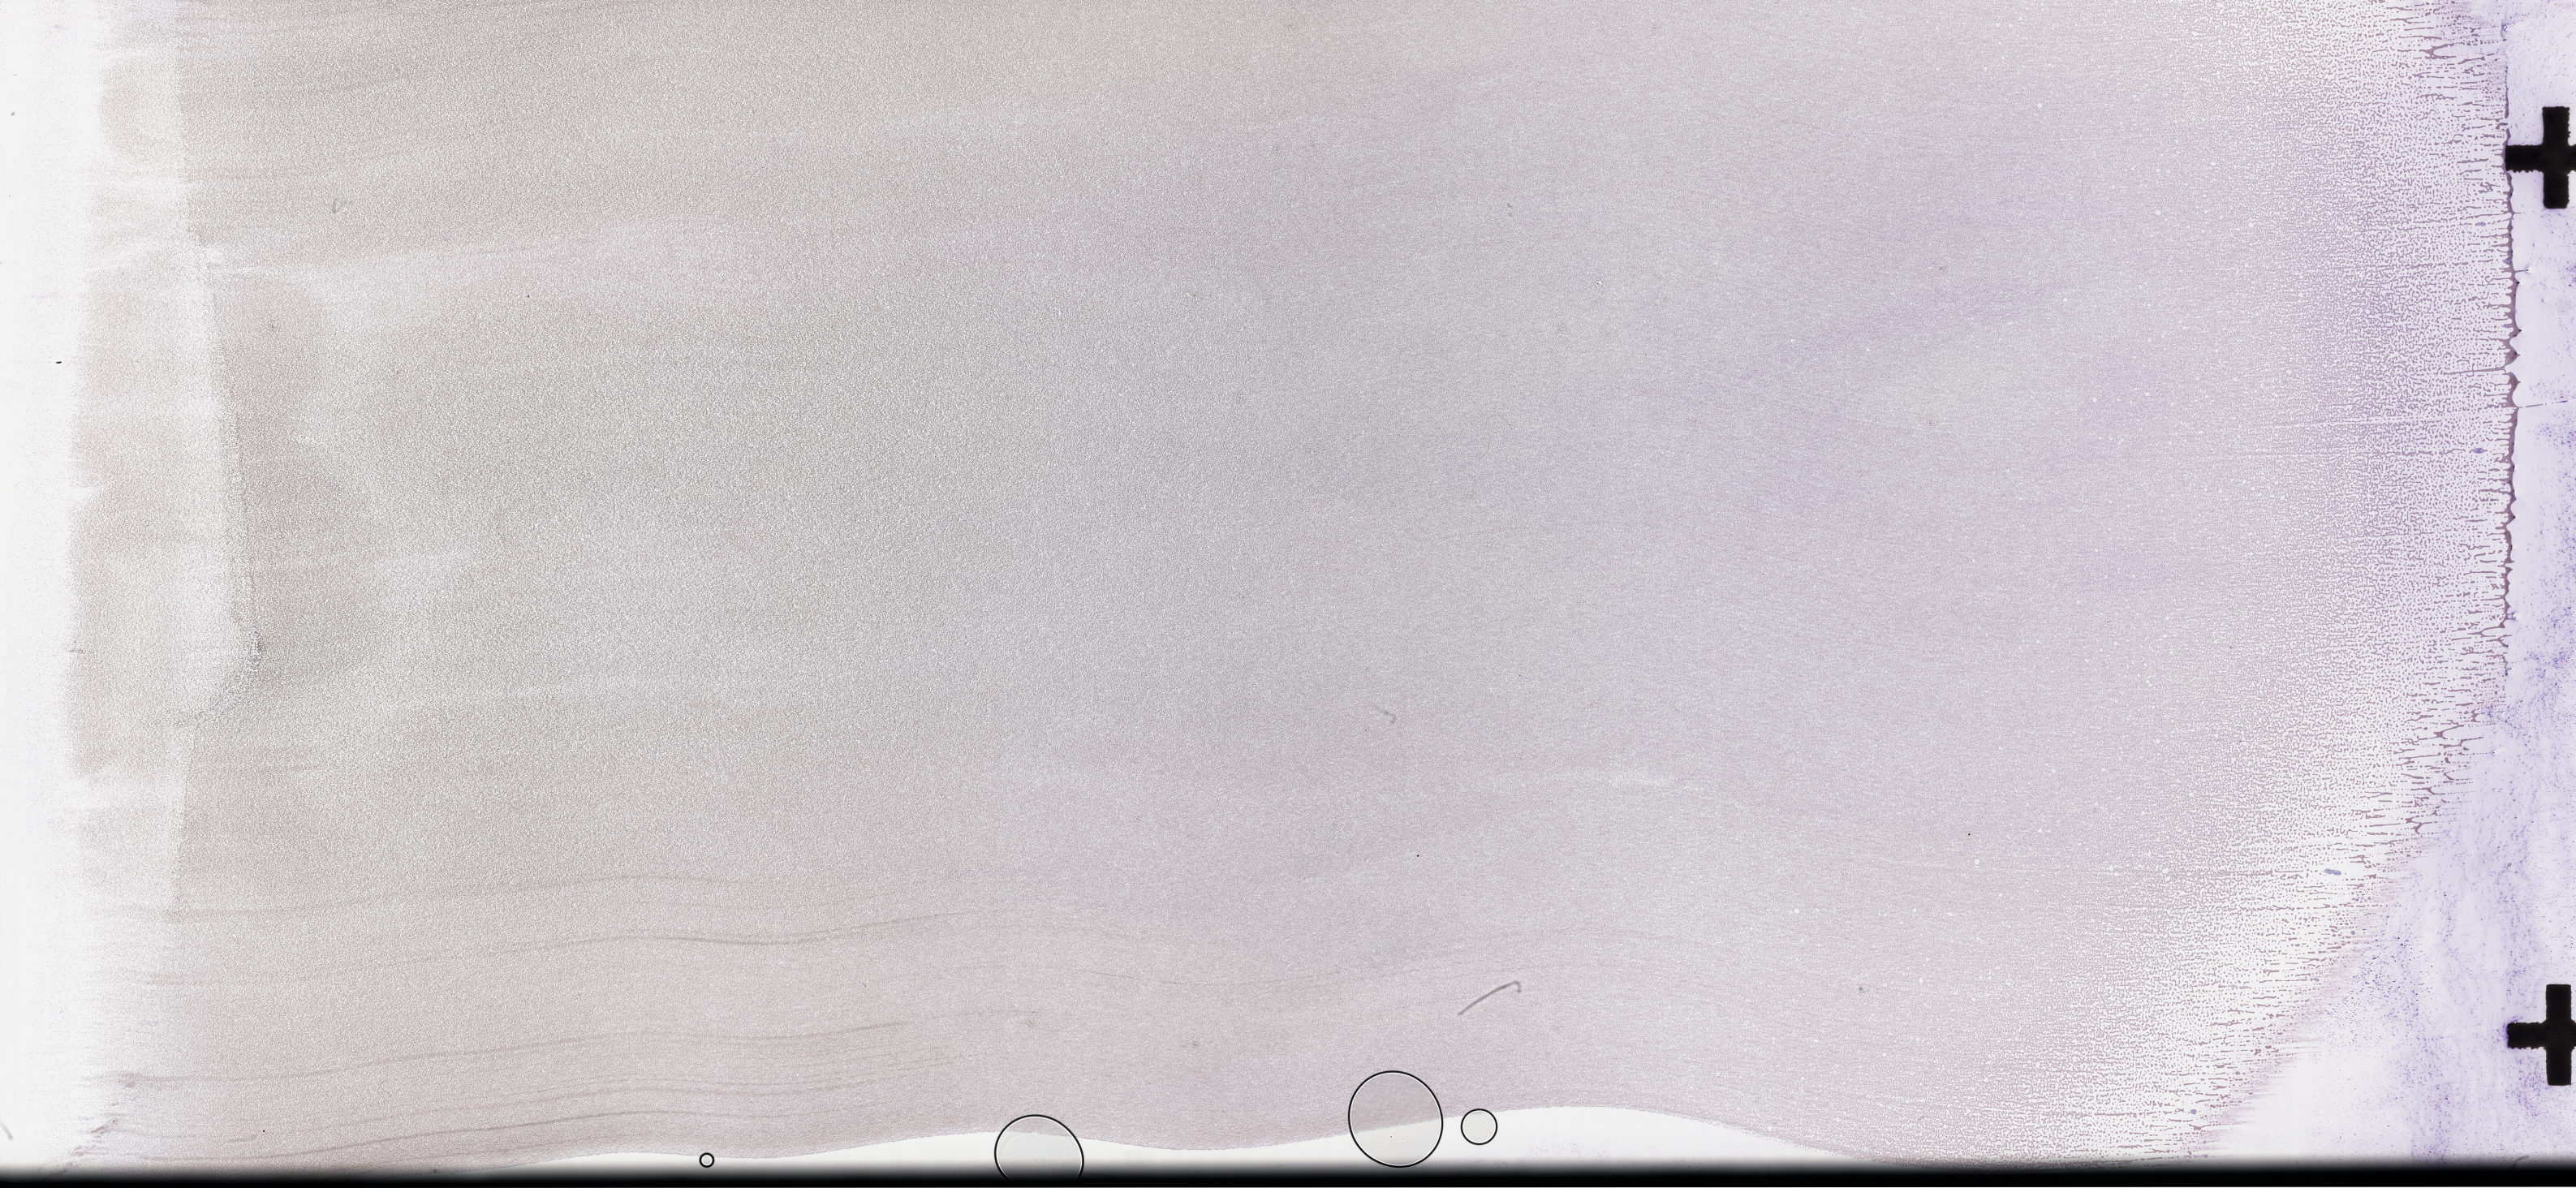
Whole-slide image of a whole blood smear, Wright-Giemsa stain — low-resolution overview of the scanned area, about 51.3 x 23.6 mm. Specimen time point: collected at disease progression. Female patient.
From a patient with: Acute Myeloid Leukemia Not Otherwise Specified.